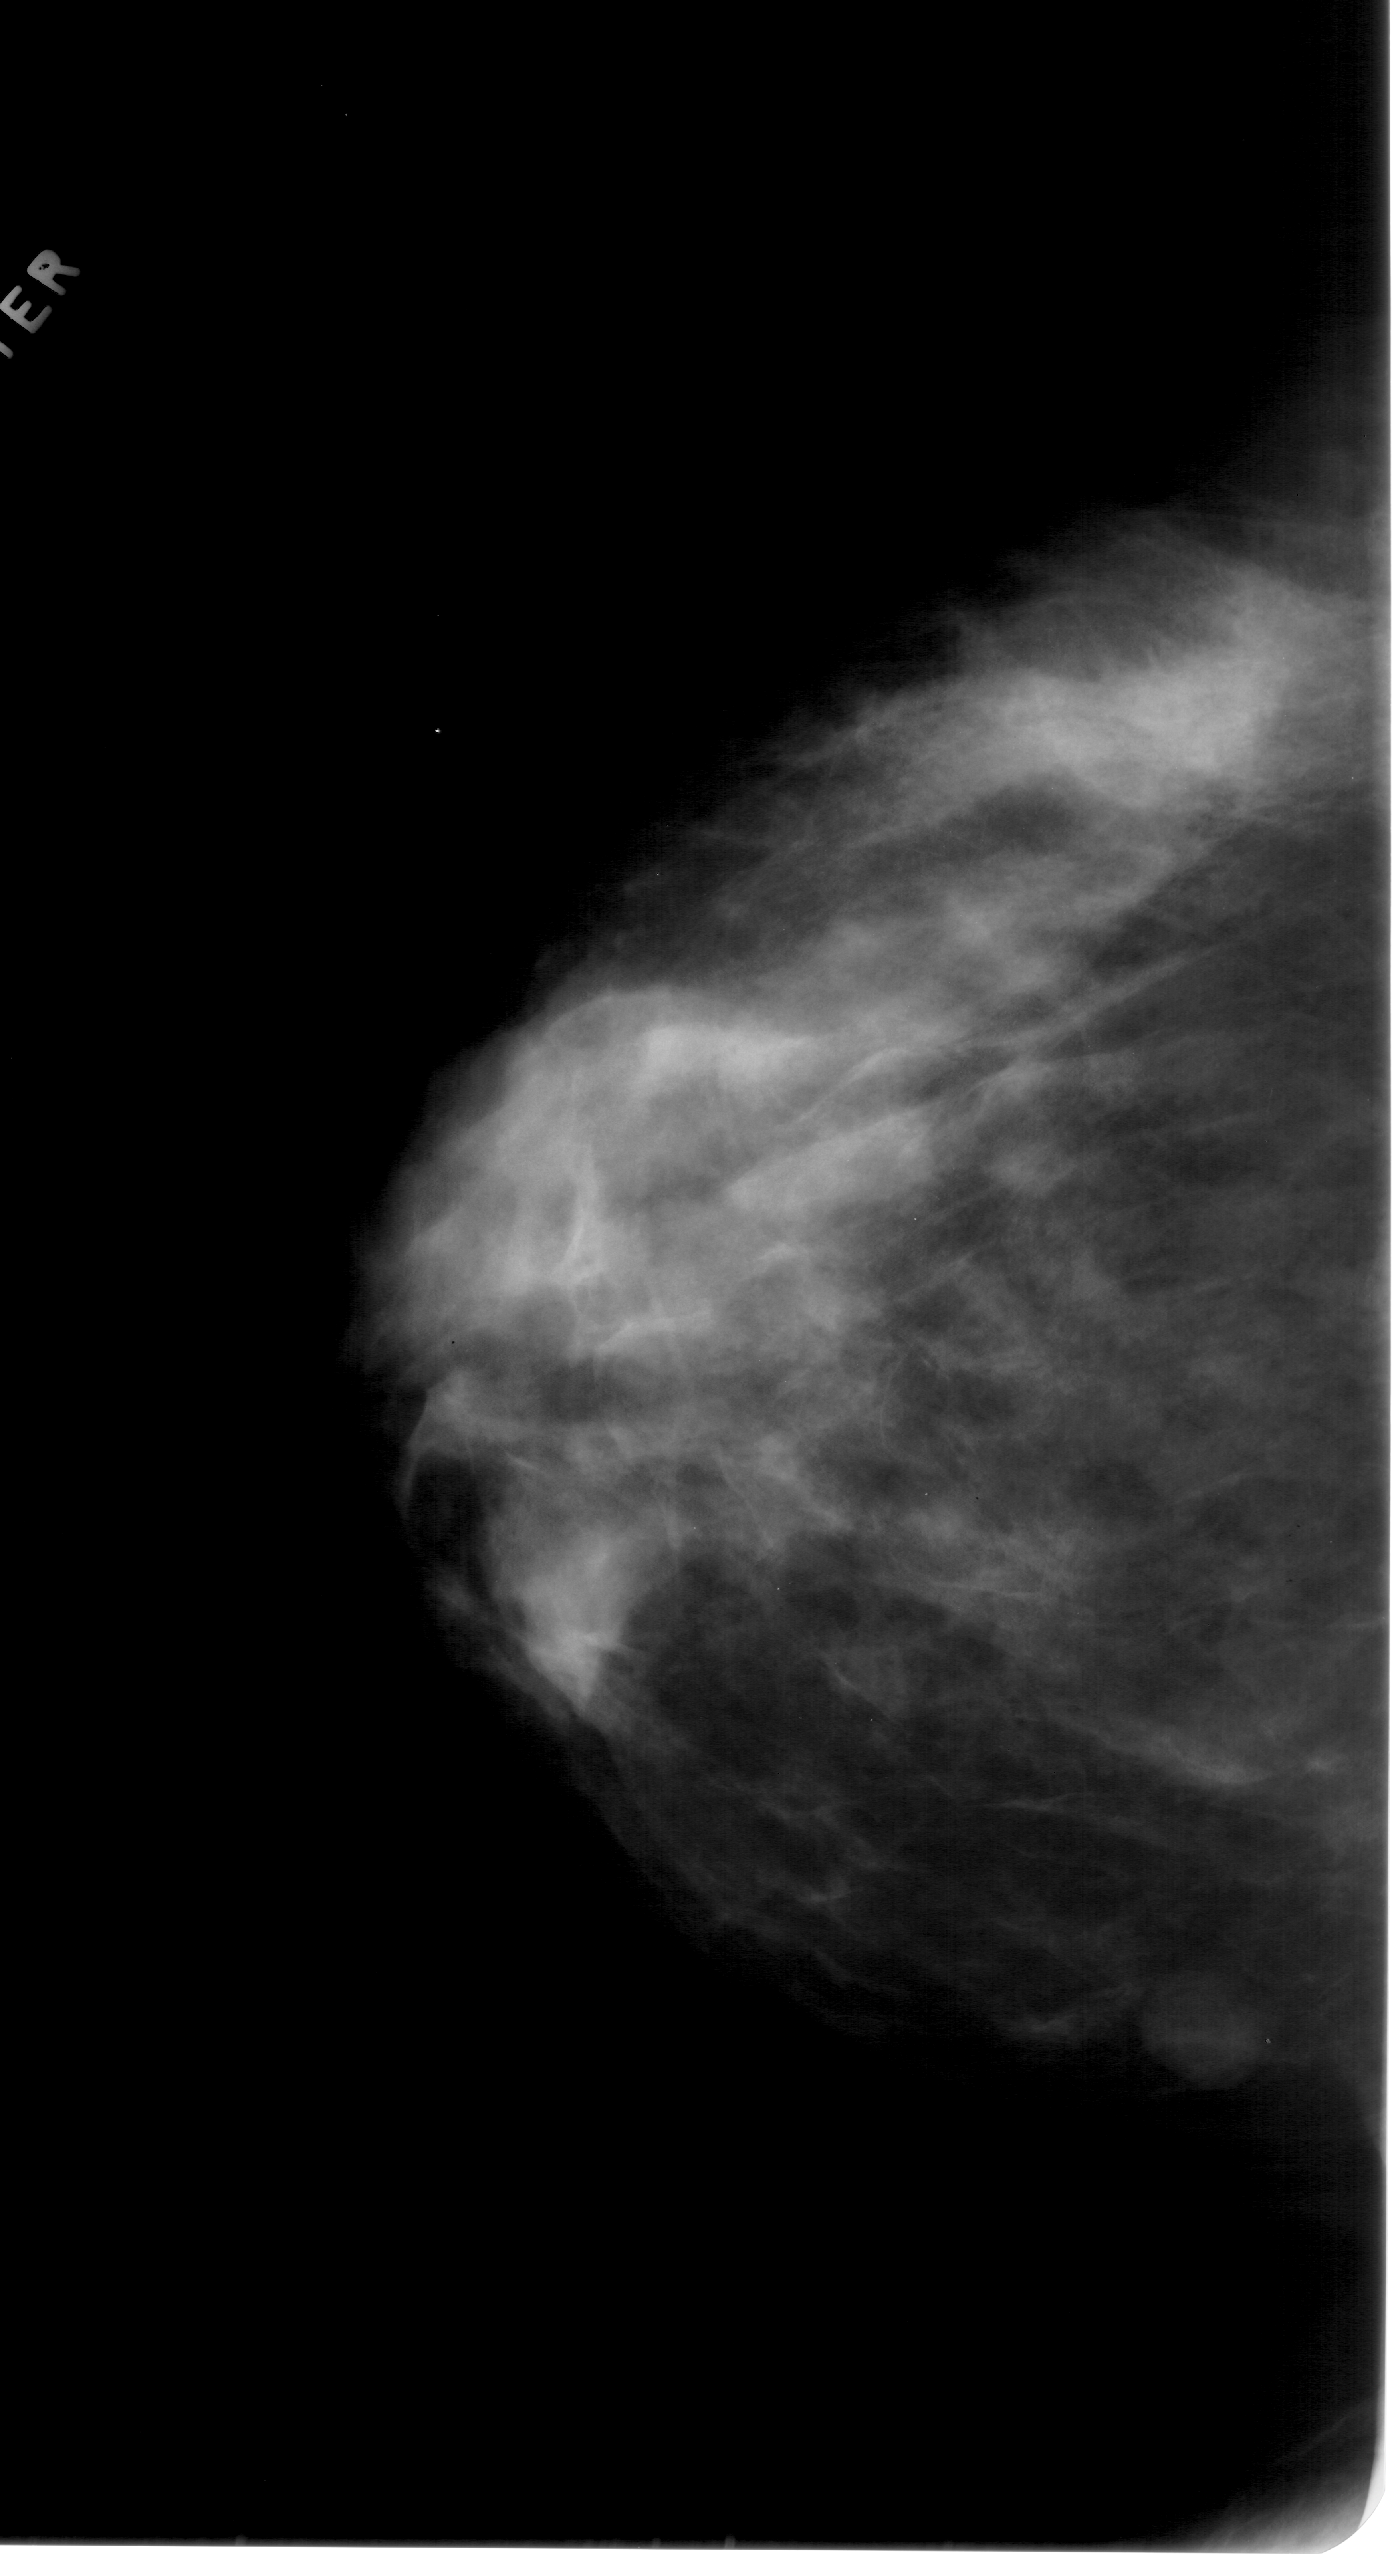
Mammogram (digitized film); left breast; craniocaudal (CC) view; 1396 × 2576 image matrix.
Expert-marked regions of interest on this image (one box per marked abnormality):
- mass, shape oval, margins circumscribed; BI-RADS assessment category 3; pathology result (as recorded, not read from the image): benign: bounding box <1146,1969,1264,2083> (left, top, right, bottom; pixels)